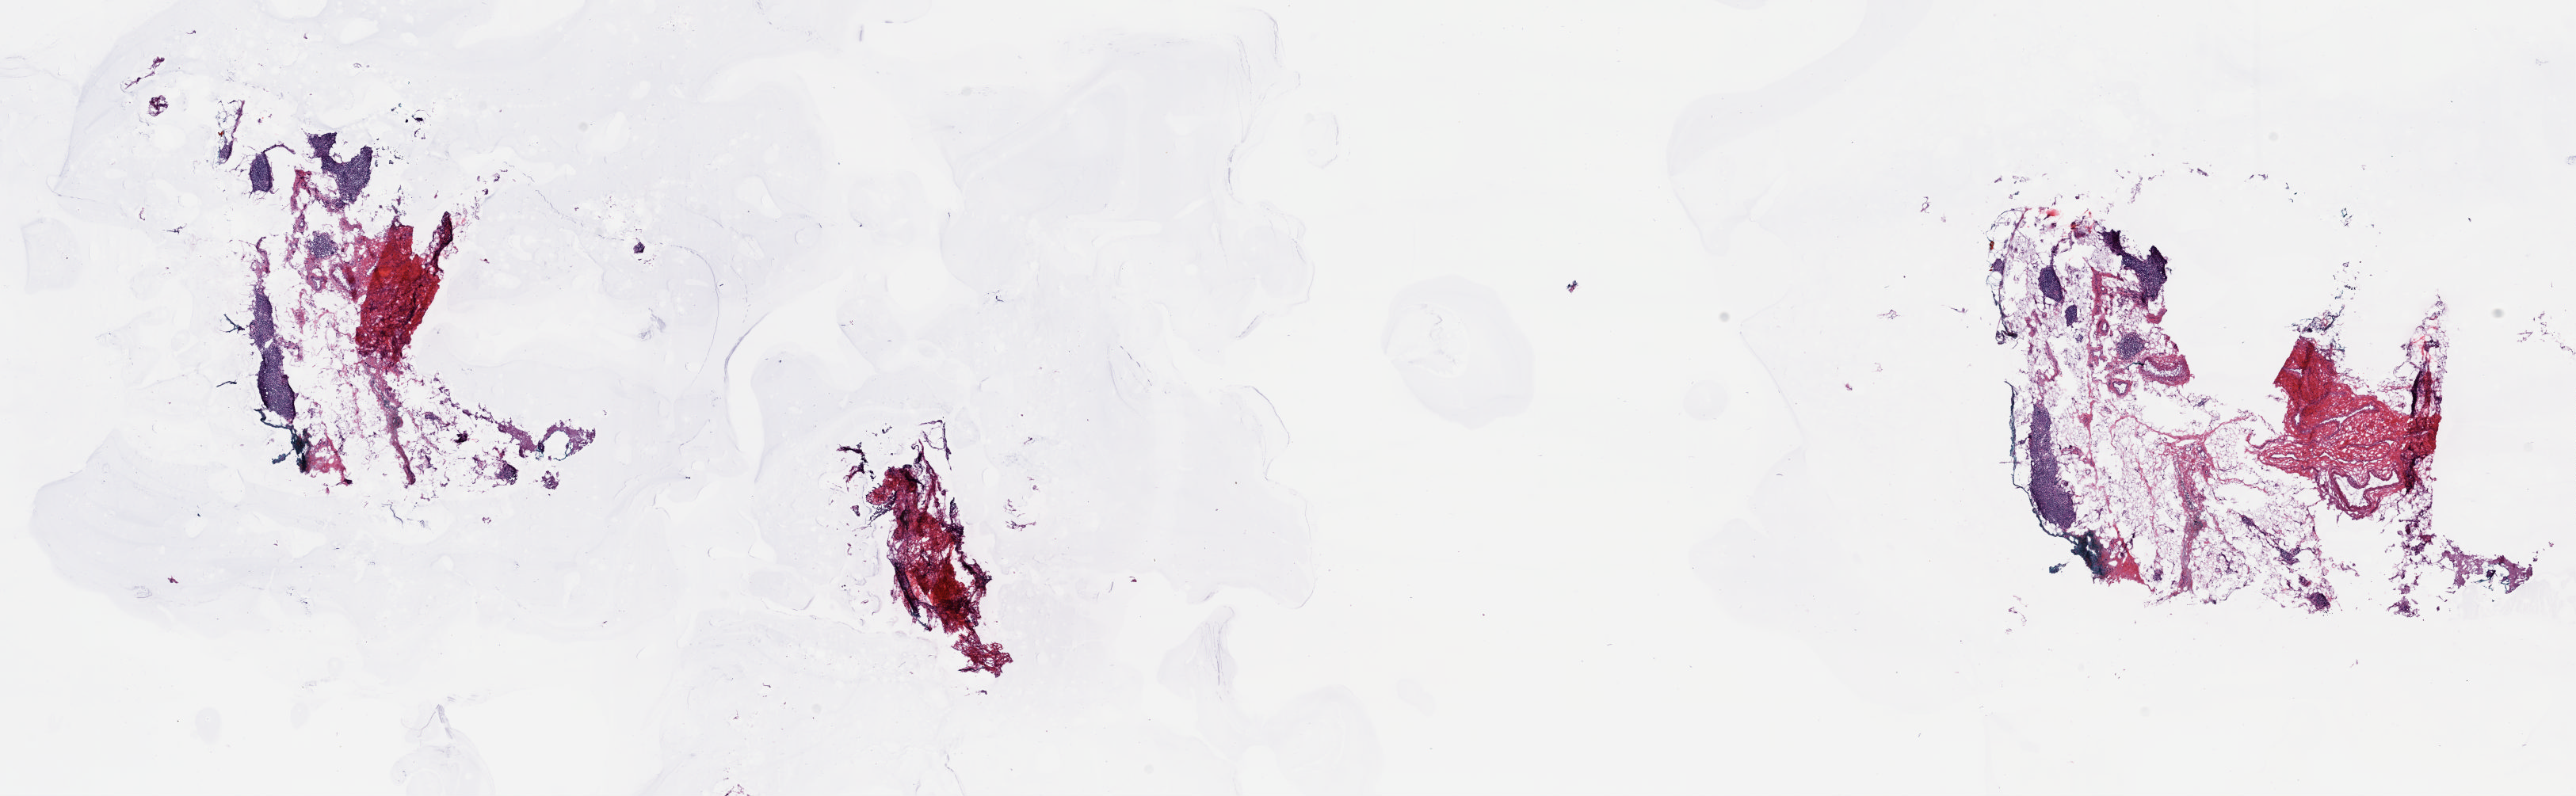
Digitized Hematoxylin and eosin (H&E) stained tissue section (whole slide) — a low-resolution overview of the entire scanned area, about 25.8 x 8.0 mm (acquisition: 20x scan). Frozen section from the top of the tissue portion. Sample: solid tissue normal (non-tumour tissue), thymus. Female patient; age at initial diagnosis 77 years. Pathologist review of this section (percent, as recorded): tumour cells 0%, tumour nuclei 0%, normal cells 100%, stromal cells 0%, necrosis 0%. Infiltration values recorded for this section: lymphocyte infiltration 0%, monocyte infiltration 0%, neutrophil infiltration 0%.
* this section: solid tissue normal sample (biorepository sample class)
* patient diagnosis: Thymoma, type AB, malignant